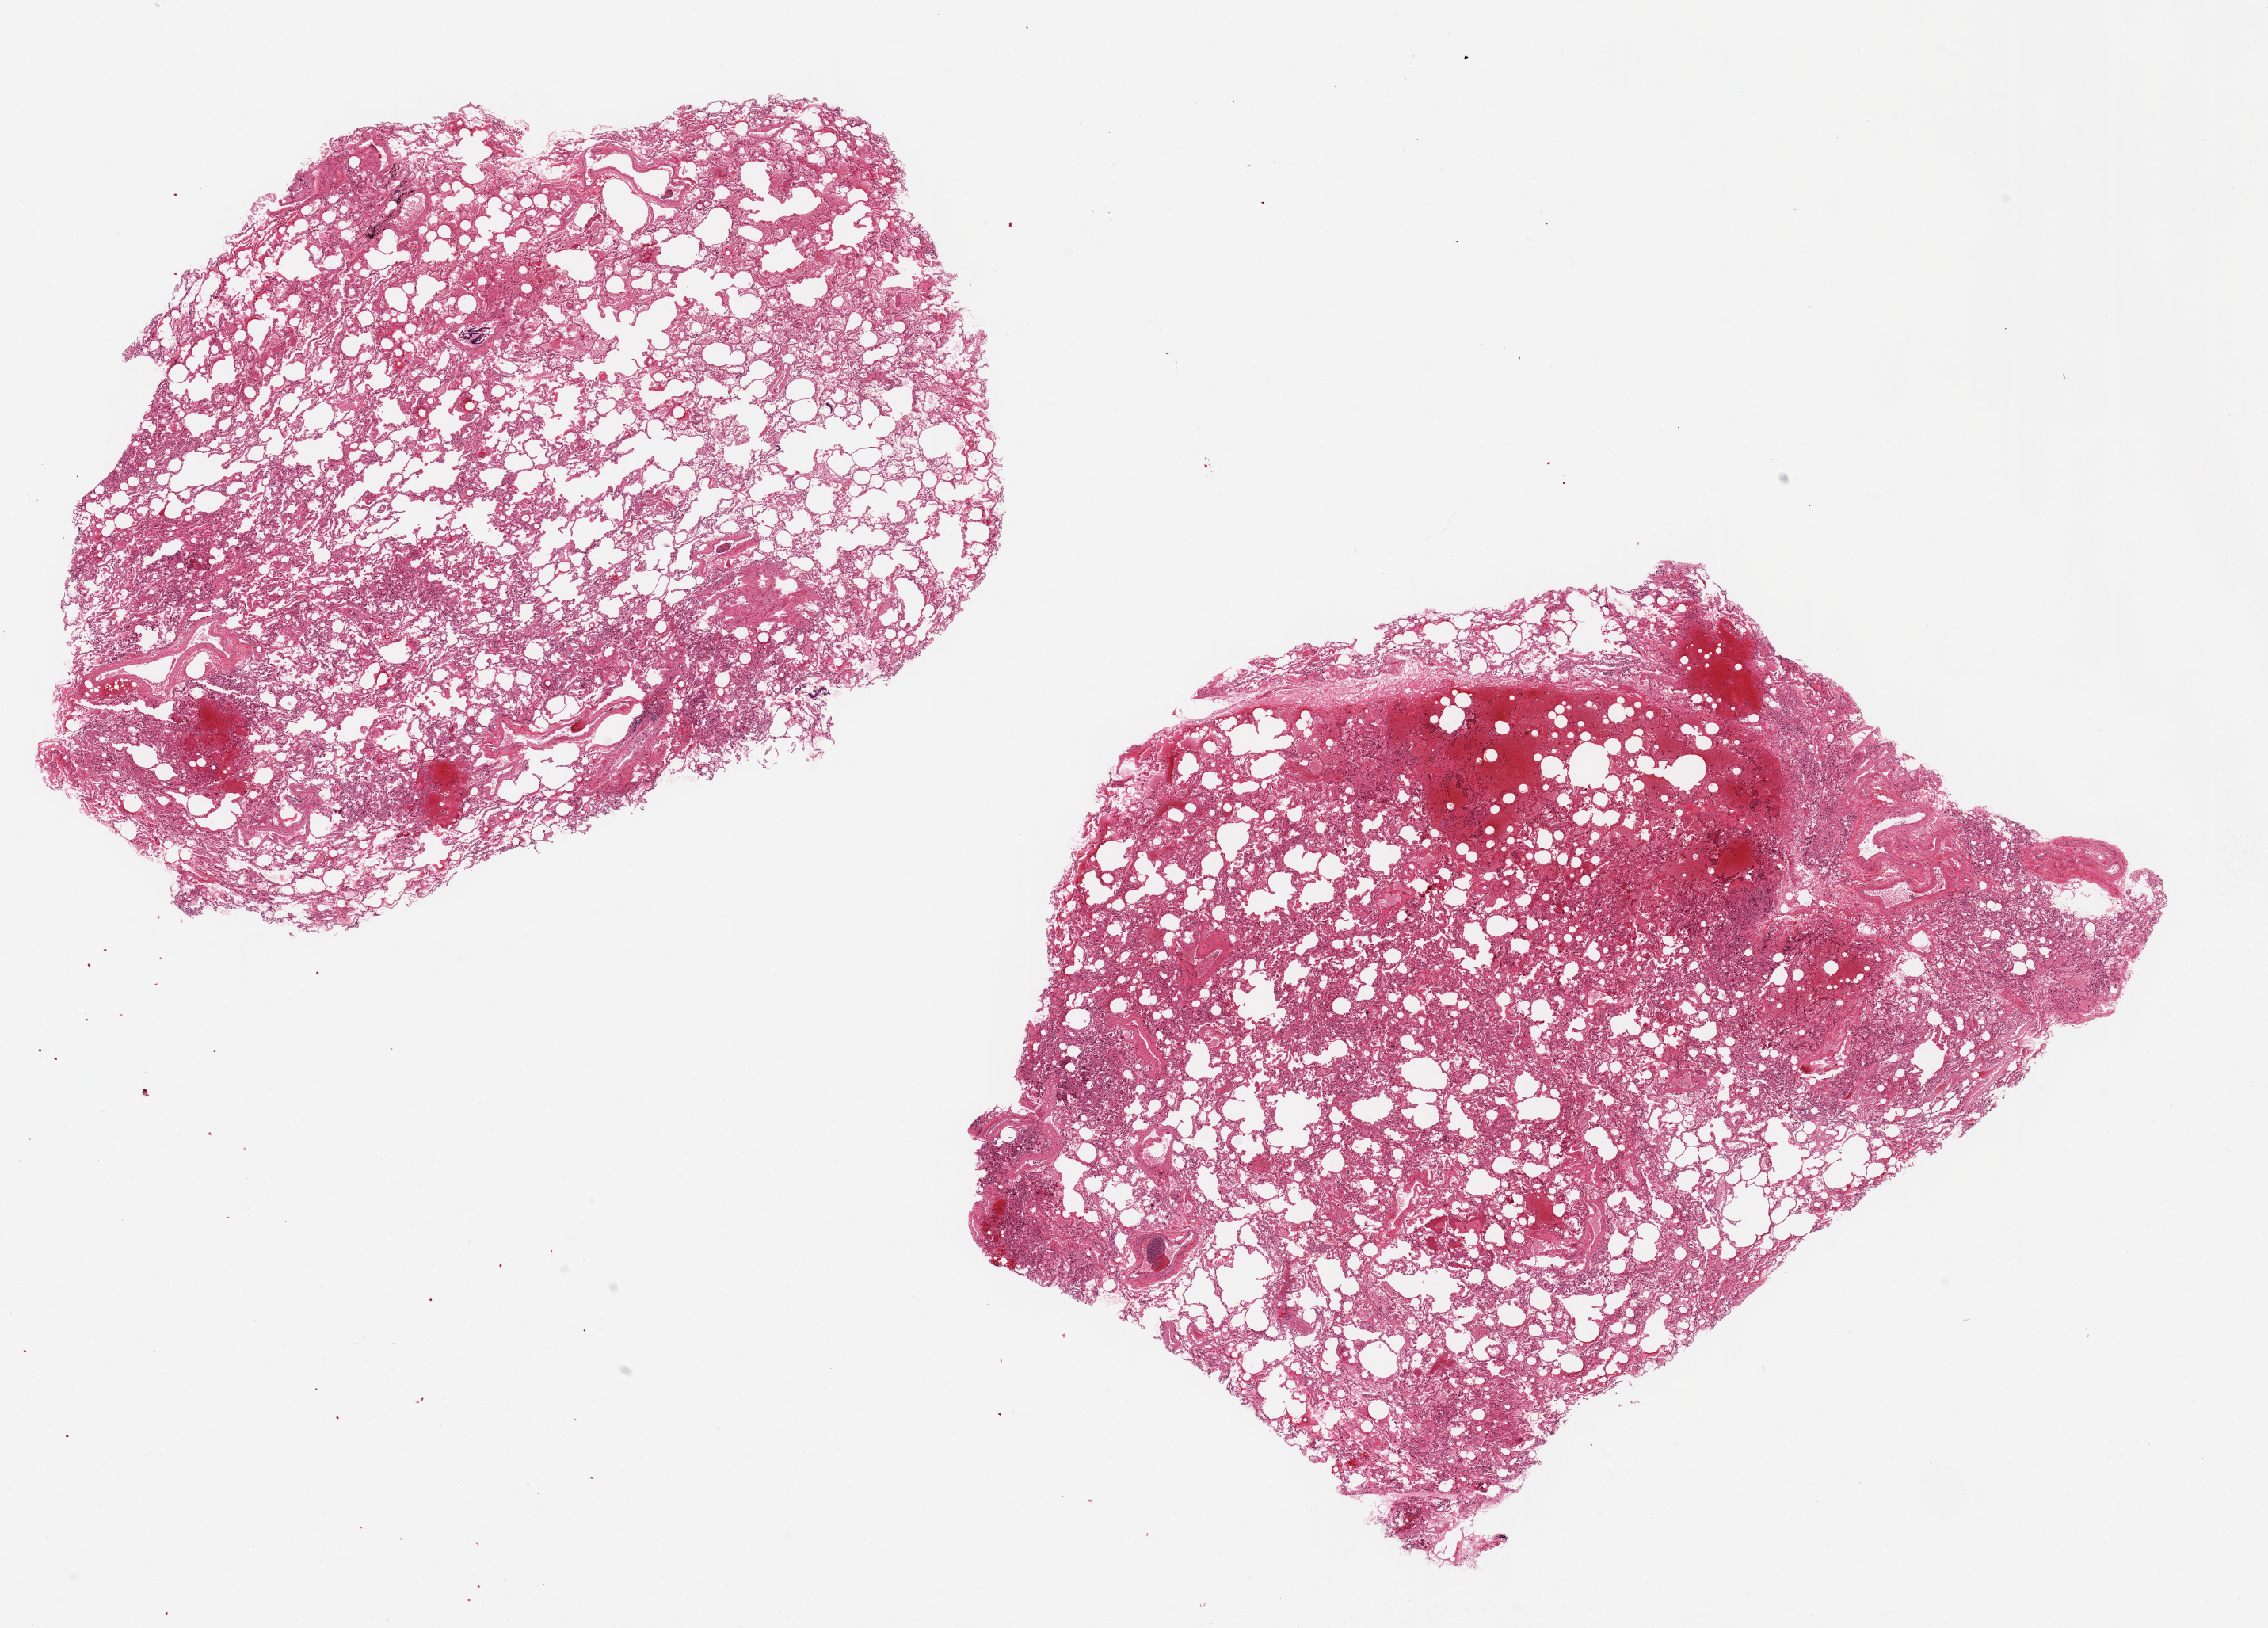
Digitized hematoxylin and eosin (H&E)-stained section — whole scanned area (about 22.6 x 16.3 mm) shown as a low-resolution overview; PAXgene-fixed paraffin-embedded (PFPE) section; target tissue: lung; donor tissue sample. Male donor.
* pathologist's review note for this sample: 2 ~10x7mm aliquots, patchy dense congestion. Bronchiolar lining badly sloughing